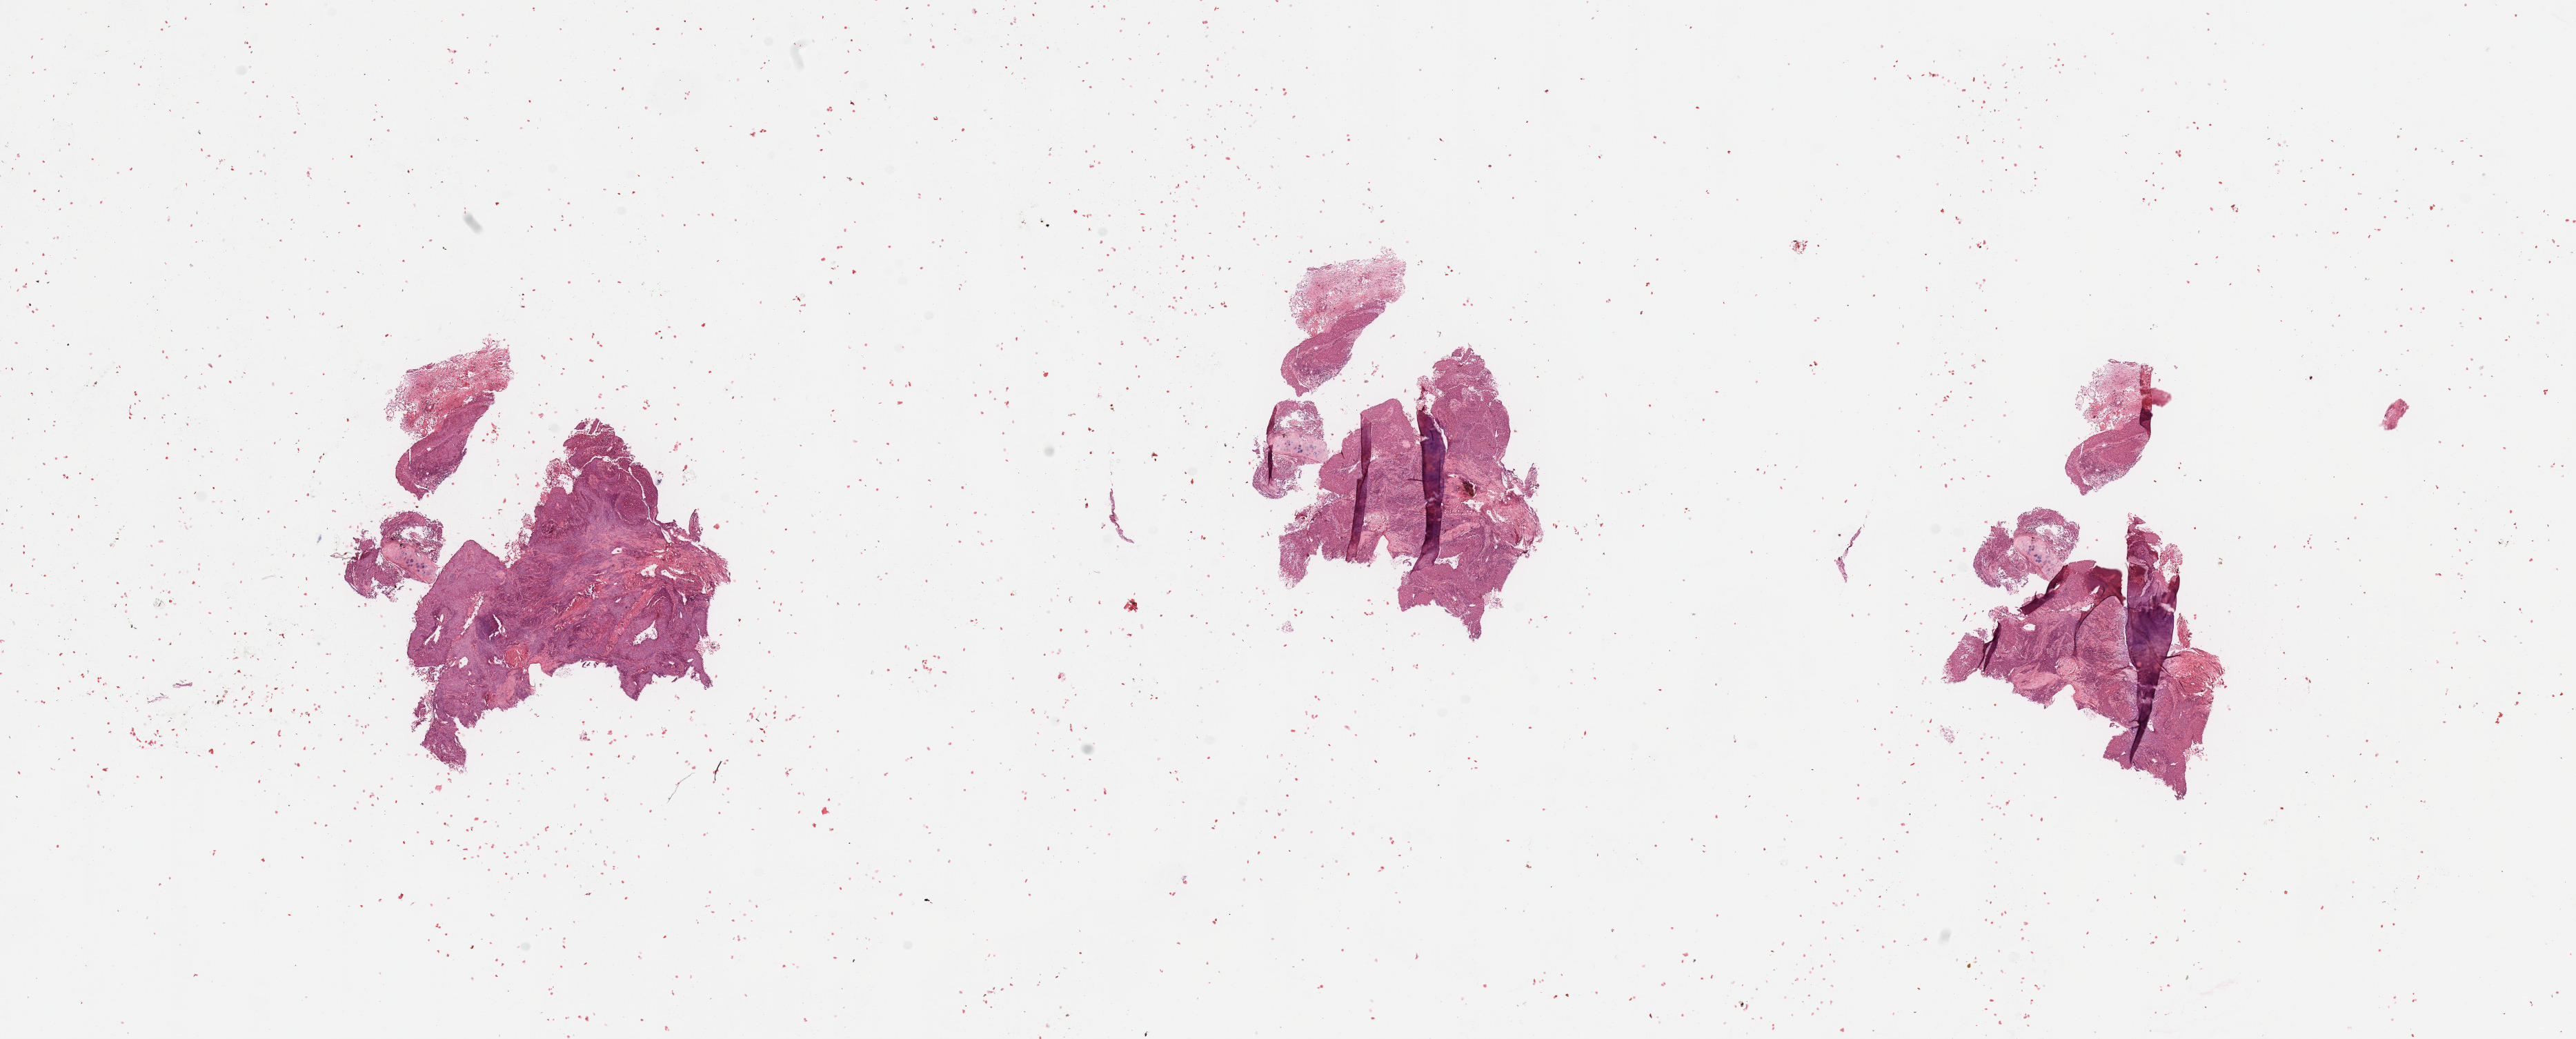
Whole-slide histology image, Hematoxylin and eosin (H&E) stained, low-resolution overview of the scanned area, about 29.5 x 11.9 mm (acquisition: 20x scan), tumour tissue sample, sampled site: lung. 63-year-old male patient. Histologic grade: G3 (poorly differentiated). Slide review estimates, as recorded: tumour nuclei 70%, necrosis 10%.
• primary tumour site (as recorded): left upper lobe
• histologic diagnosis: Squamous cell carcinoma, NOS
• AJCC pathologic stage: IIIA